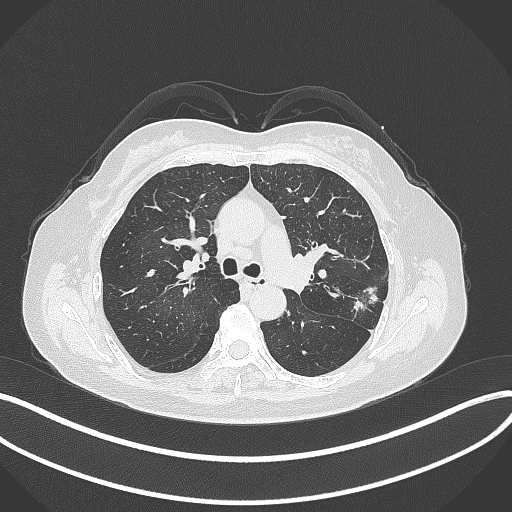
Chest CT, one axial slice; slice 206 of 319 in the series (ordered by position); reconstruction kernel B70f; lung window (W 1500 / L -600 HU); 1 mm slice thickness; 512 × 512 image matrix, field of view 400 × 400 mm. Patient: female, 60 years. From the clinical record (not read from this slice): clinical TNM (as recorded): T1c N0 M0.
Annotated regions visible in this slice (bounding box drawn by a radiologist):
- lung tumour (recorded histology: adenocarcinoma): bounding box (x1, y1, x2, y2) in pixels: (348, 281, 379, 320)